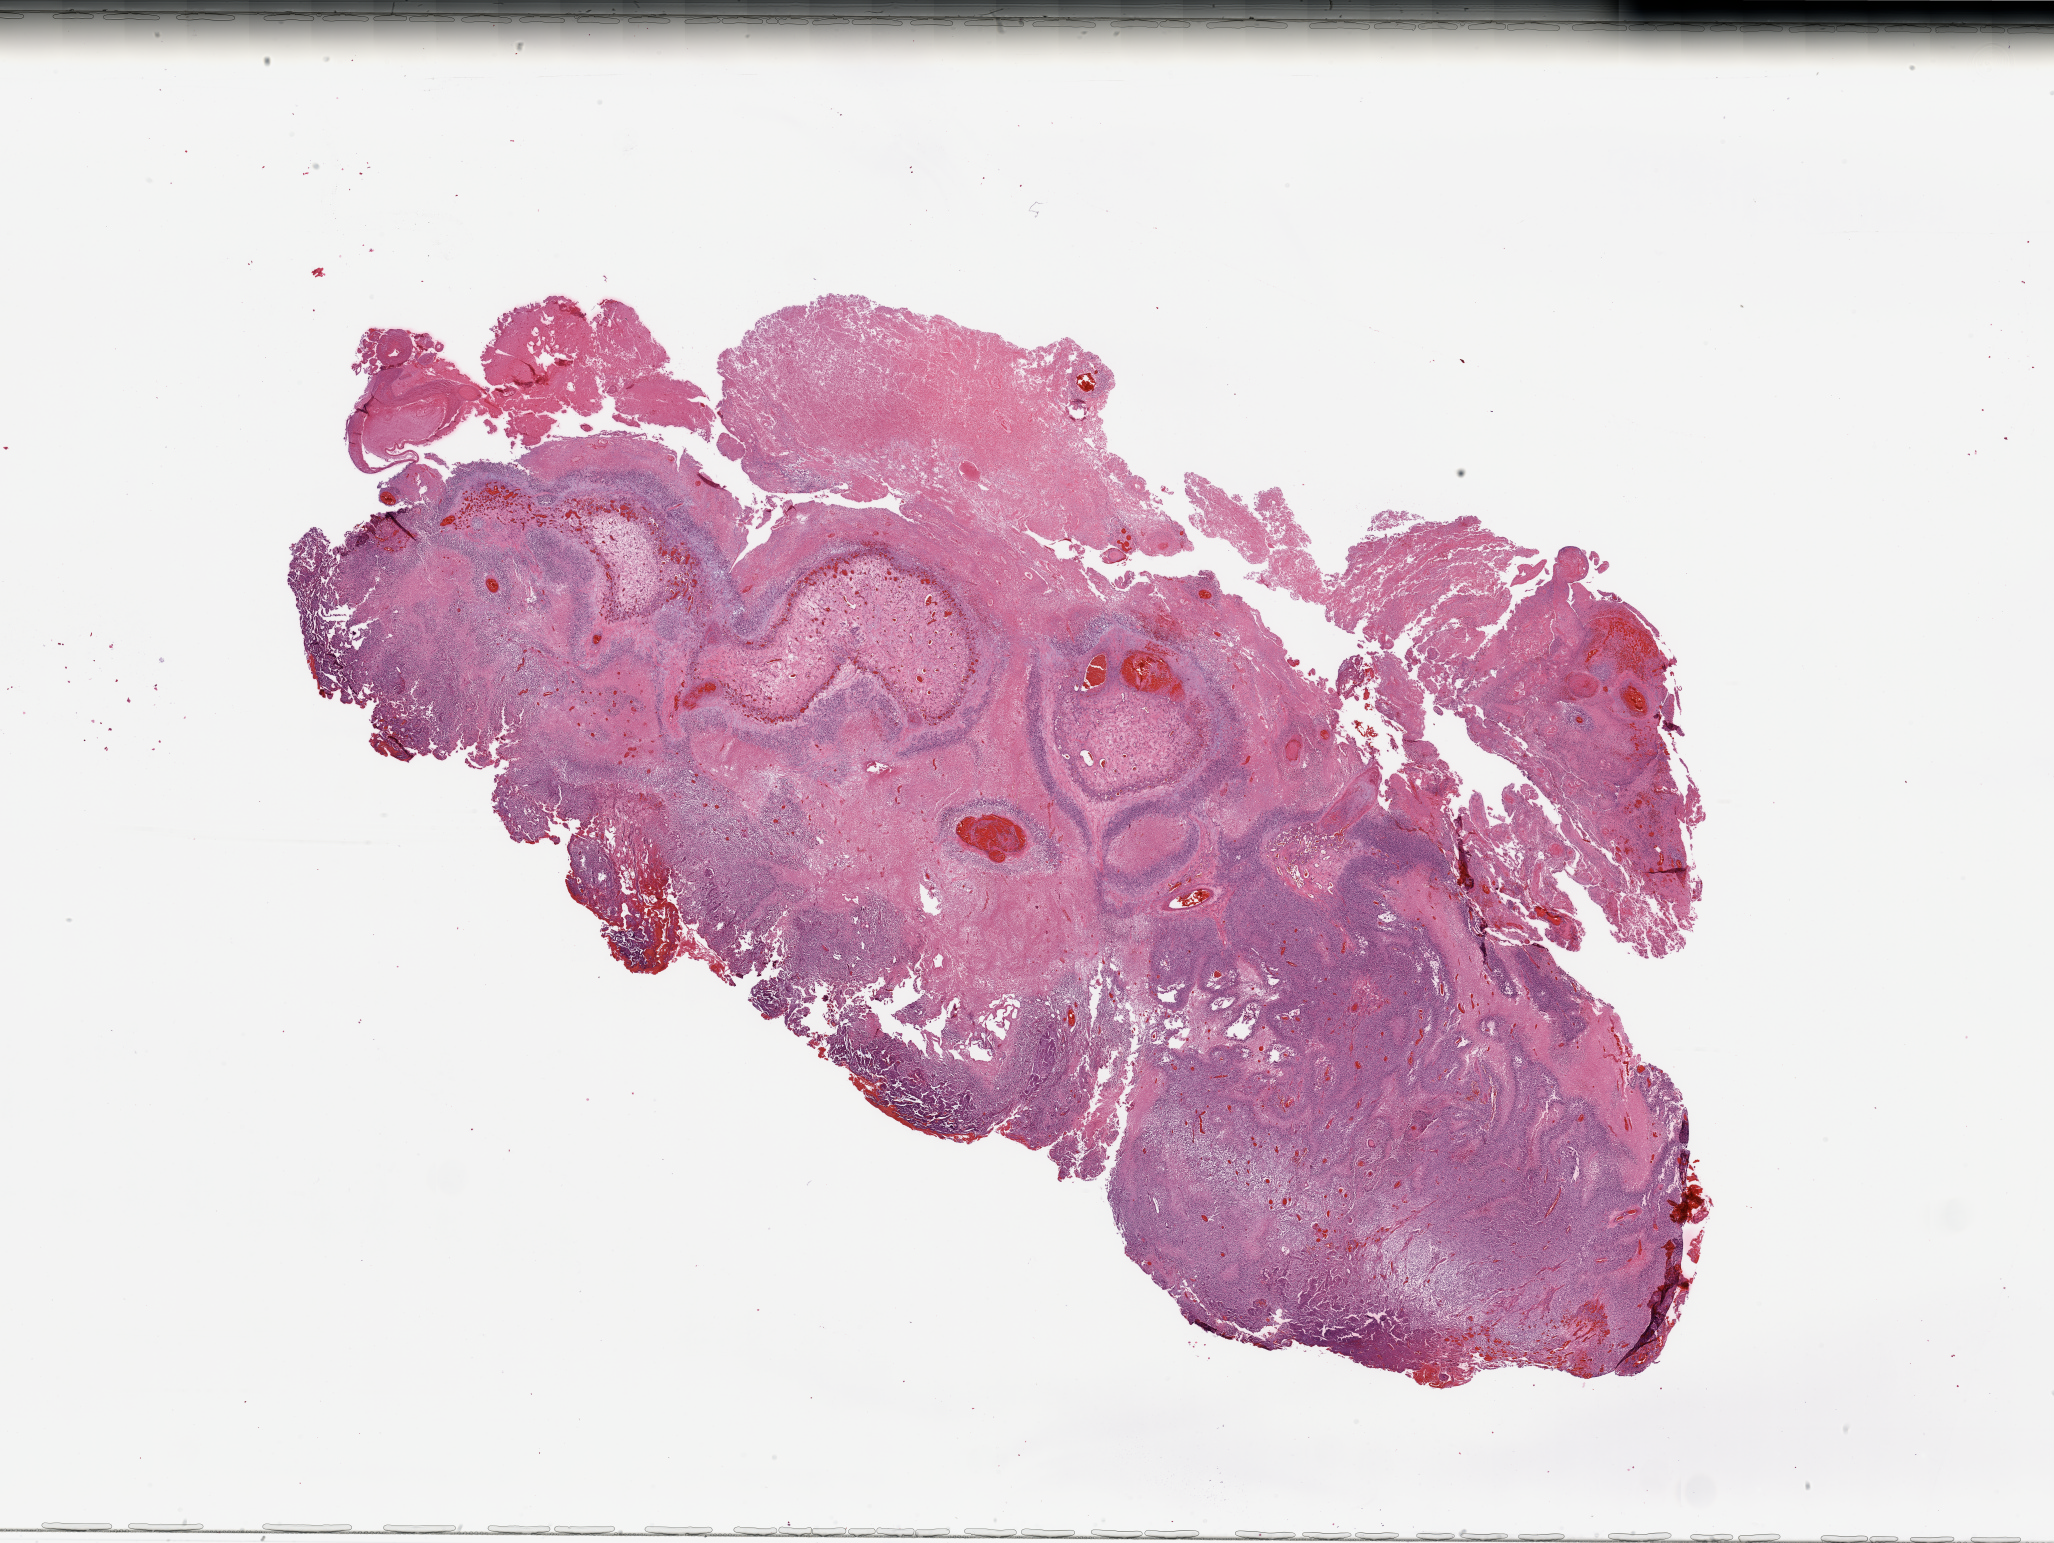
H&E whole-slide image — whole scanned area (about 32.5 x 24.4 mm) shown as a low-resolution overview; tumour tissue sample, brain. Patient: male, age 62 years.
Primary tumour site (as recorded): frontal lobe. Patient diagnosis (cohort enrolment): glioblastoma multiforme (brain).